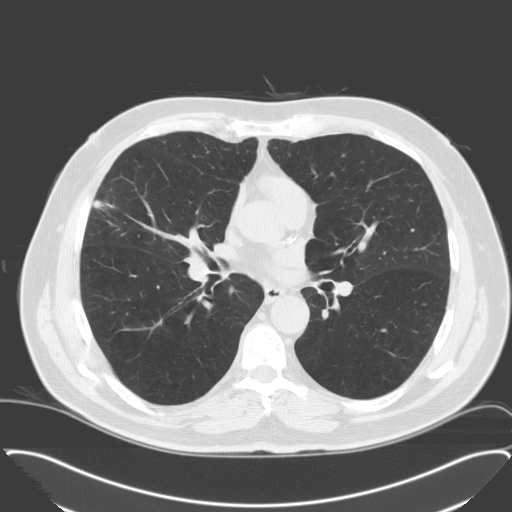
Low-dose screening chest CT, one axial slice. Position 95 of 174 along the scan axis. 120 kVp. Lung window (W 1500 / L -600 HU). 3.2 mm slice thickness. 512 × 512 image matrix.
Annotated regions visible in this slice (expert manual segmentation):
- lesion 1 (tumor, middle lobe of right lung): bounding box <92,200,114,210> (left, top, right, bottom; pixels)